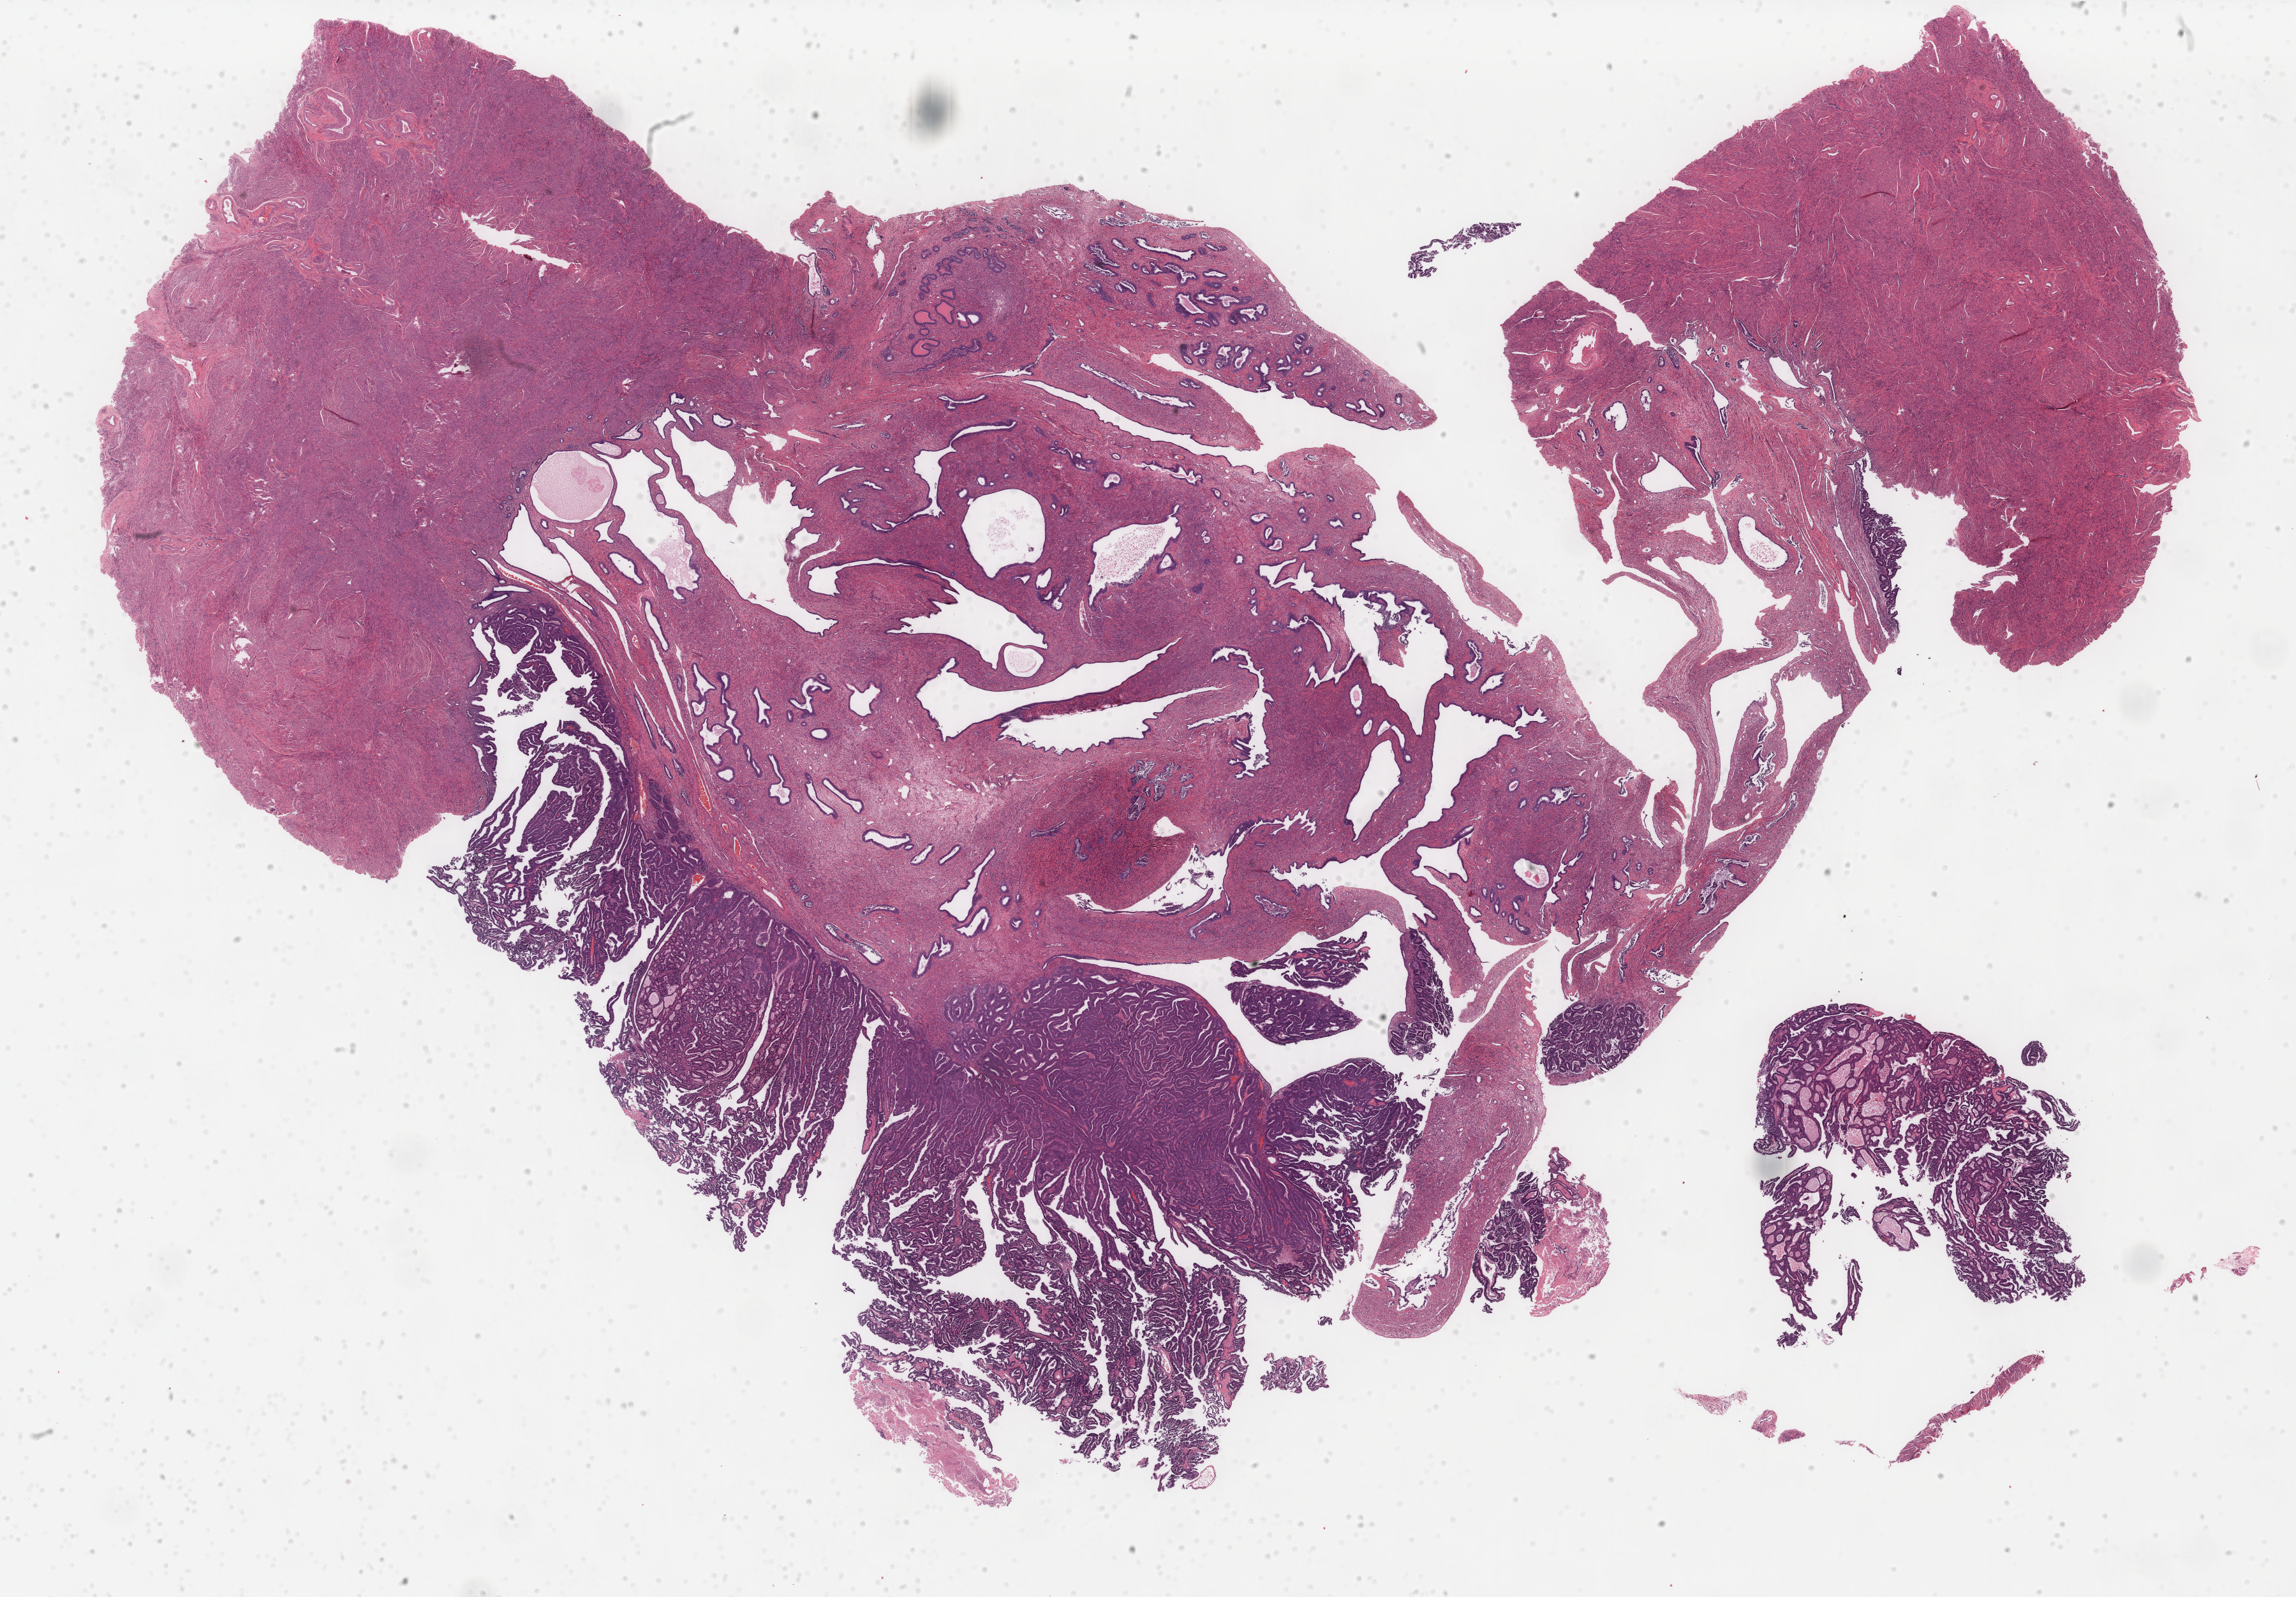
Digitized H&E tissue section (whole slide) — shown as a low-resolution overview of the whole scanned area (about 28.6 x 19.9 mm). FFPE section. Primary tumour sample from the uterus. Patient: female, age at initial diagnosis 72 years. Histologic grade: G3 (poorly differentiated).
* FIGO stage: IVB
* histologic diagnosis: Serous cystadenocarcinoma, NOS (endometrium)